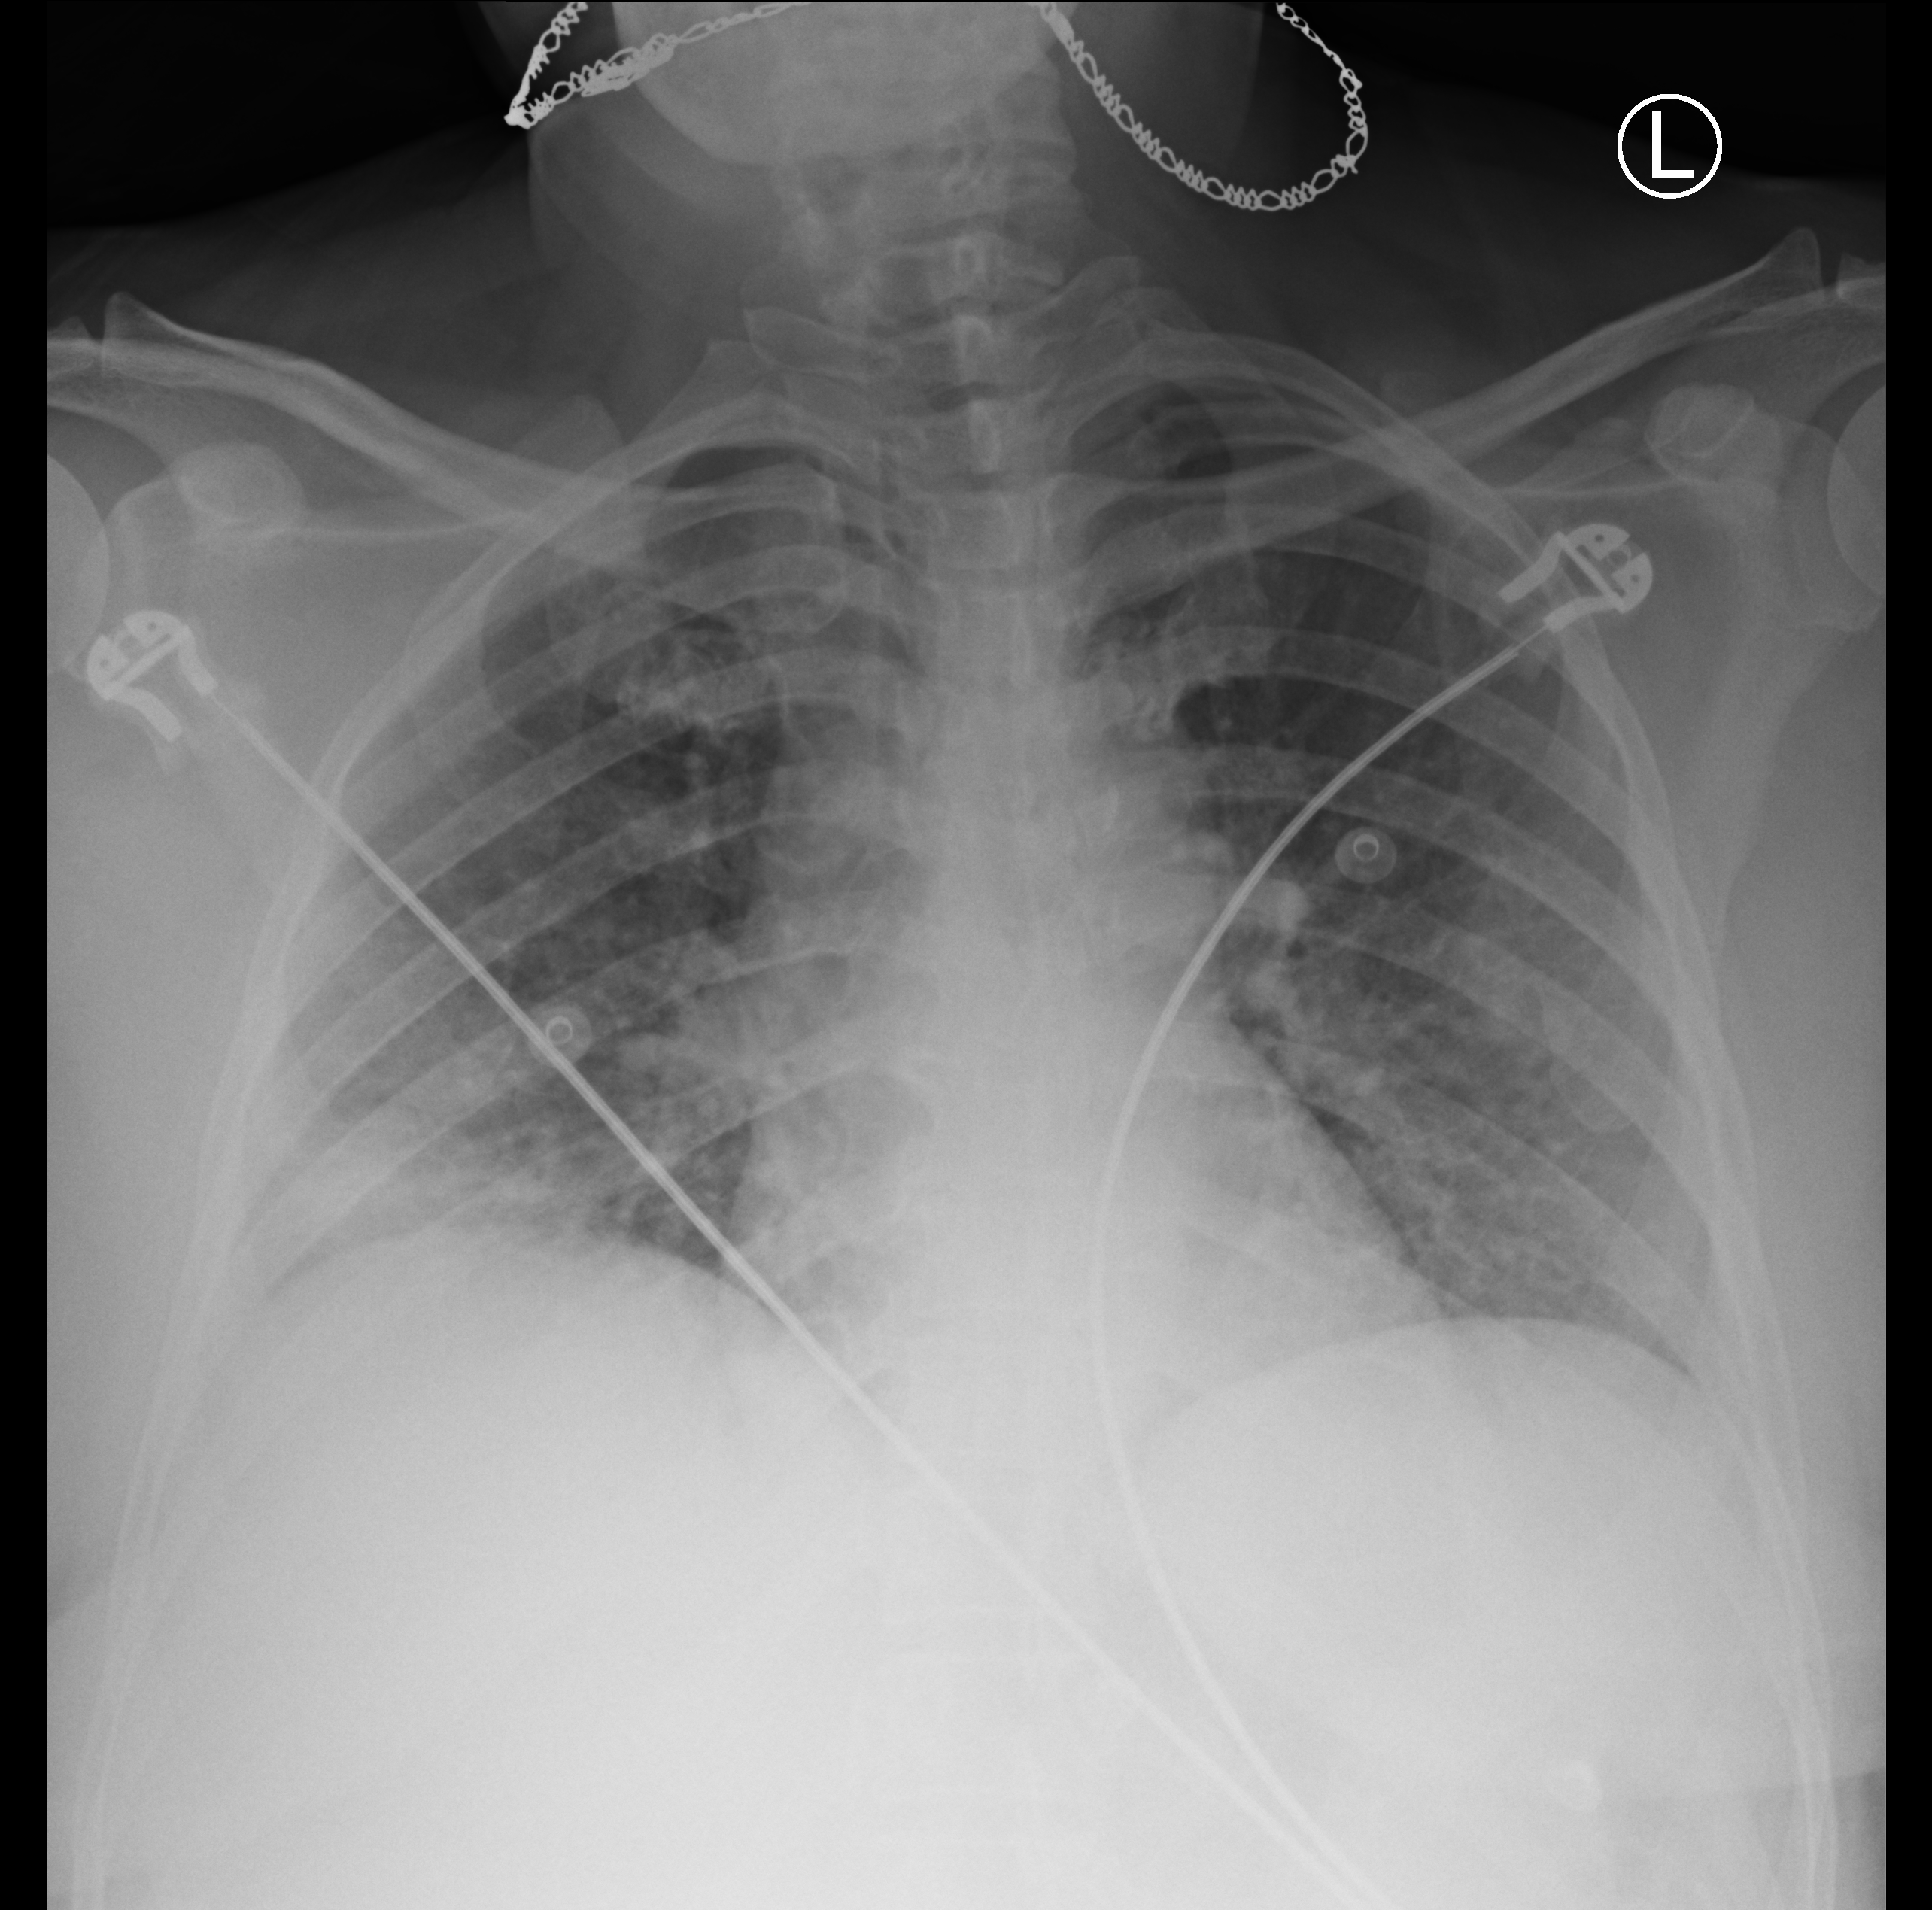
Bedside chest radiograph (computed radiography); anteroposterior (AP) projection. Patient hospitalised with COVID-19; female, aged 18–59 years.
Hospital-stay facts (about this admission, not read from this image; timing relative to this image not recorded):
- length of hospital stay: 5 days